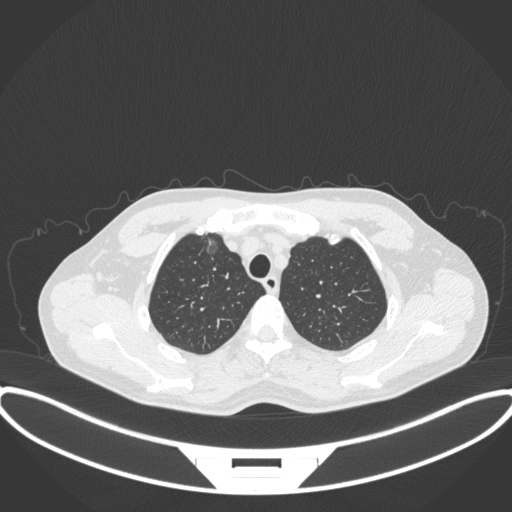
Chest CT, one axial slice. Slice 305 of 395 in the series (ordered by position). 120 kVp. Lung window (W 1500 / L -600 HU). 512 × 512 image matrix, field of view 424 × 424 mm. Male patient, age 60 years. From the clinical record (not read from this slice): clinical TNM (as recorded): T1c N0 M0.
Annotated regions visible in this slice (bounding box drawn by a radiologist):
- lung tumour (recorded histology: adenocarcinoma): box from (x=203, y=230) to (x=220, y=257) px